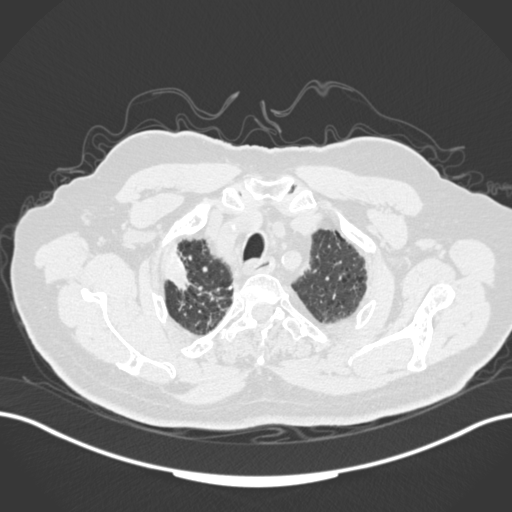
Chest CT, one axial slice; slice 148 of 205 in the series (ordered by position); reconstruction kernel B30f; 120 kVp; lung window (W 1500 / L -600 HU); 512 × 512 image matrix, field of view 400 × 400 mm. Patient: male, 72 years. From the clinical record (not read from this slice): clinical TNM (as recorded): T1a N0 M0.
Structures marked on this image (bounding box drawn by a radiologist):
- lung tumour (recorded histology: squamous cell carcinoma): bounding box (x1, y1, x2, y2) in pixels: (162, 239, 195, 293)